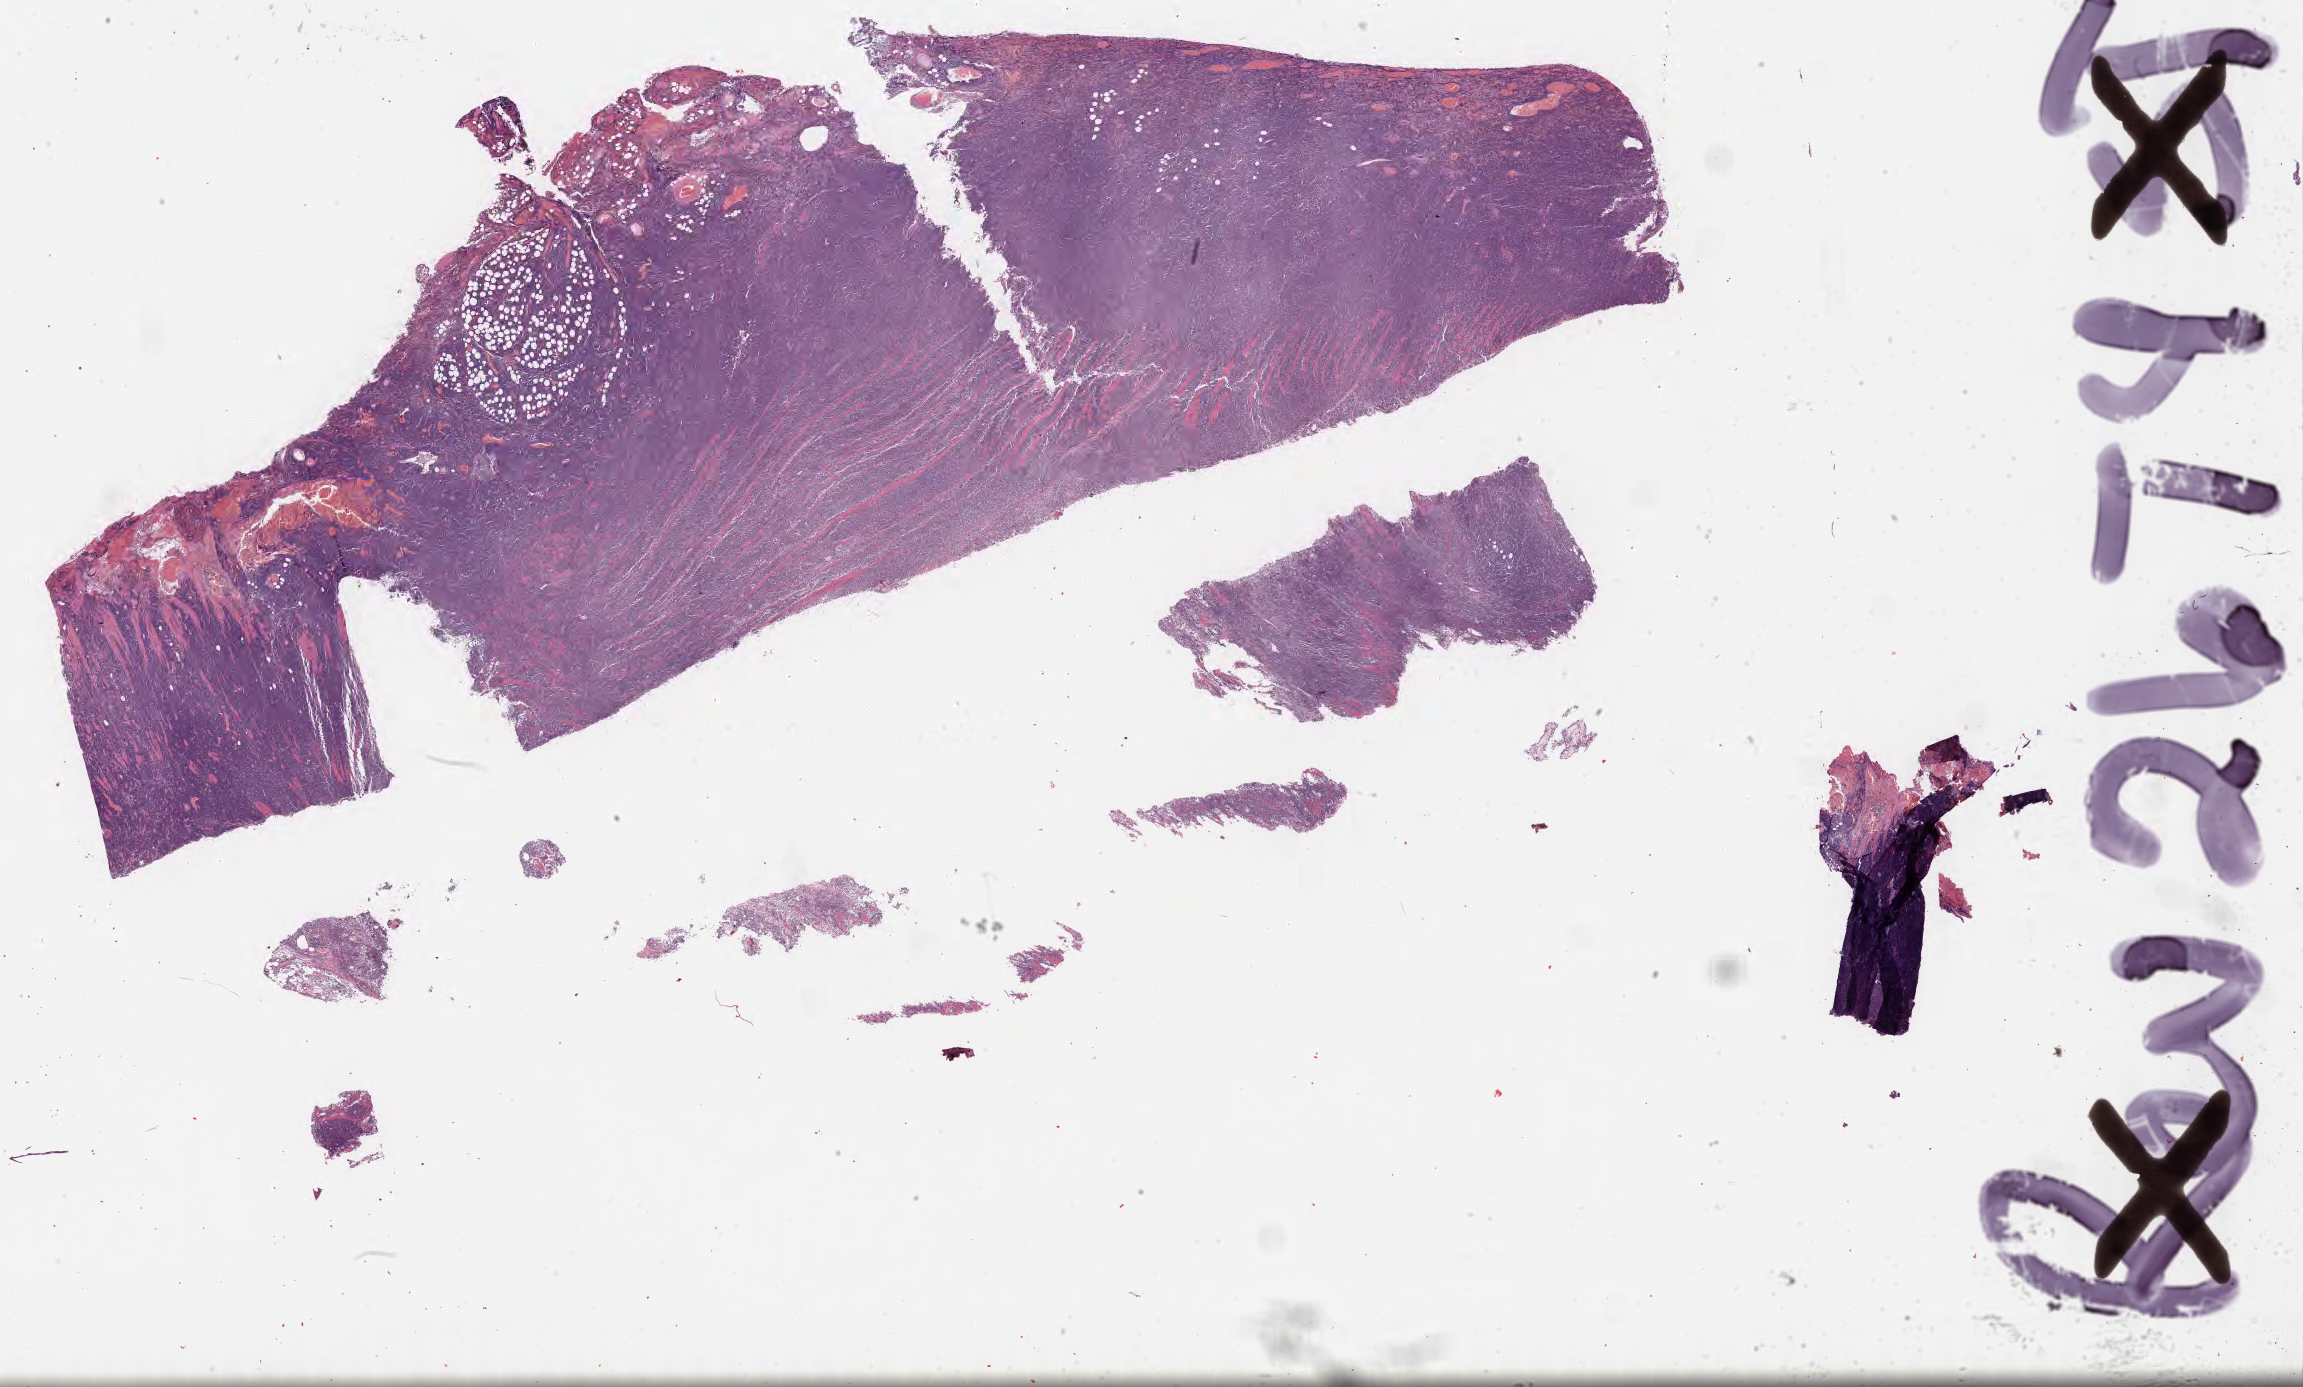
Whole-slide image, haematoxylin and eosin stain — low-resolution overview of the scanned area, about 37.2 x 22.4 mm. Specimen: tumor tissue. Patient male; age 56 years.
Diagnosis: Burkitt lymphoma, NOS.